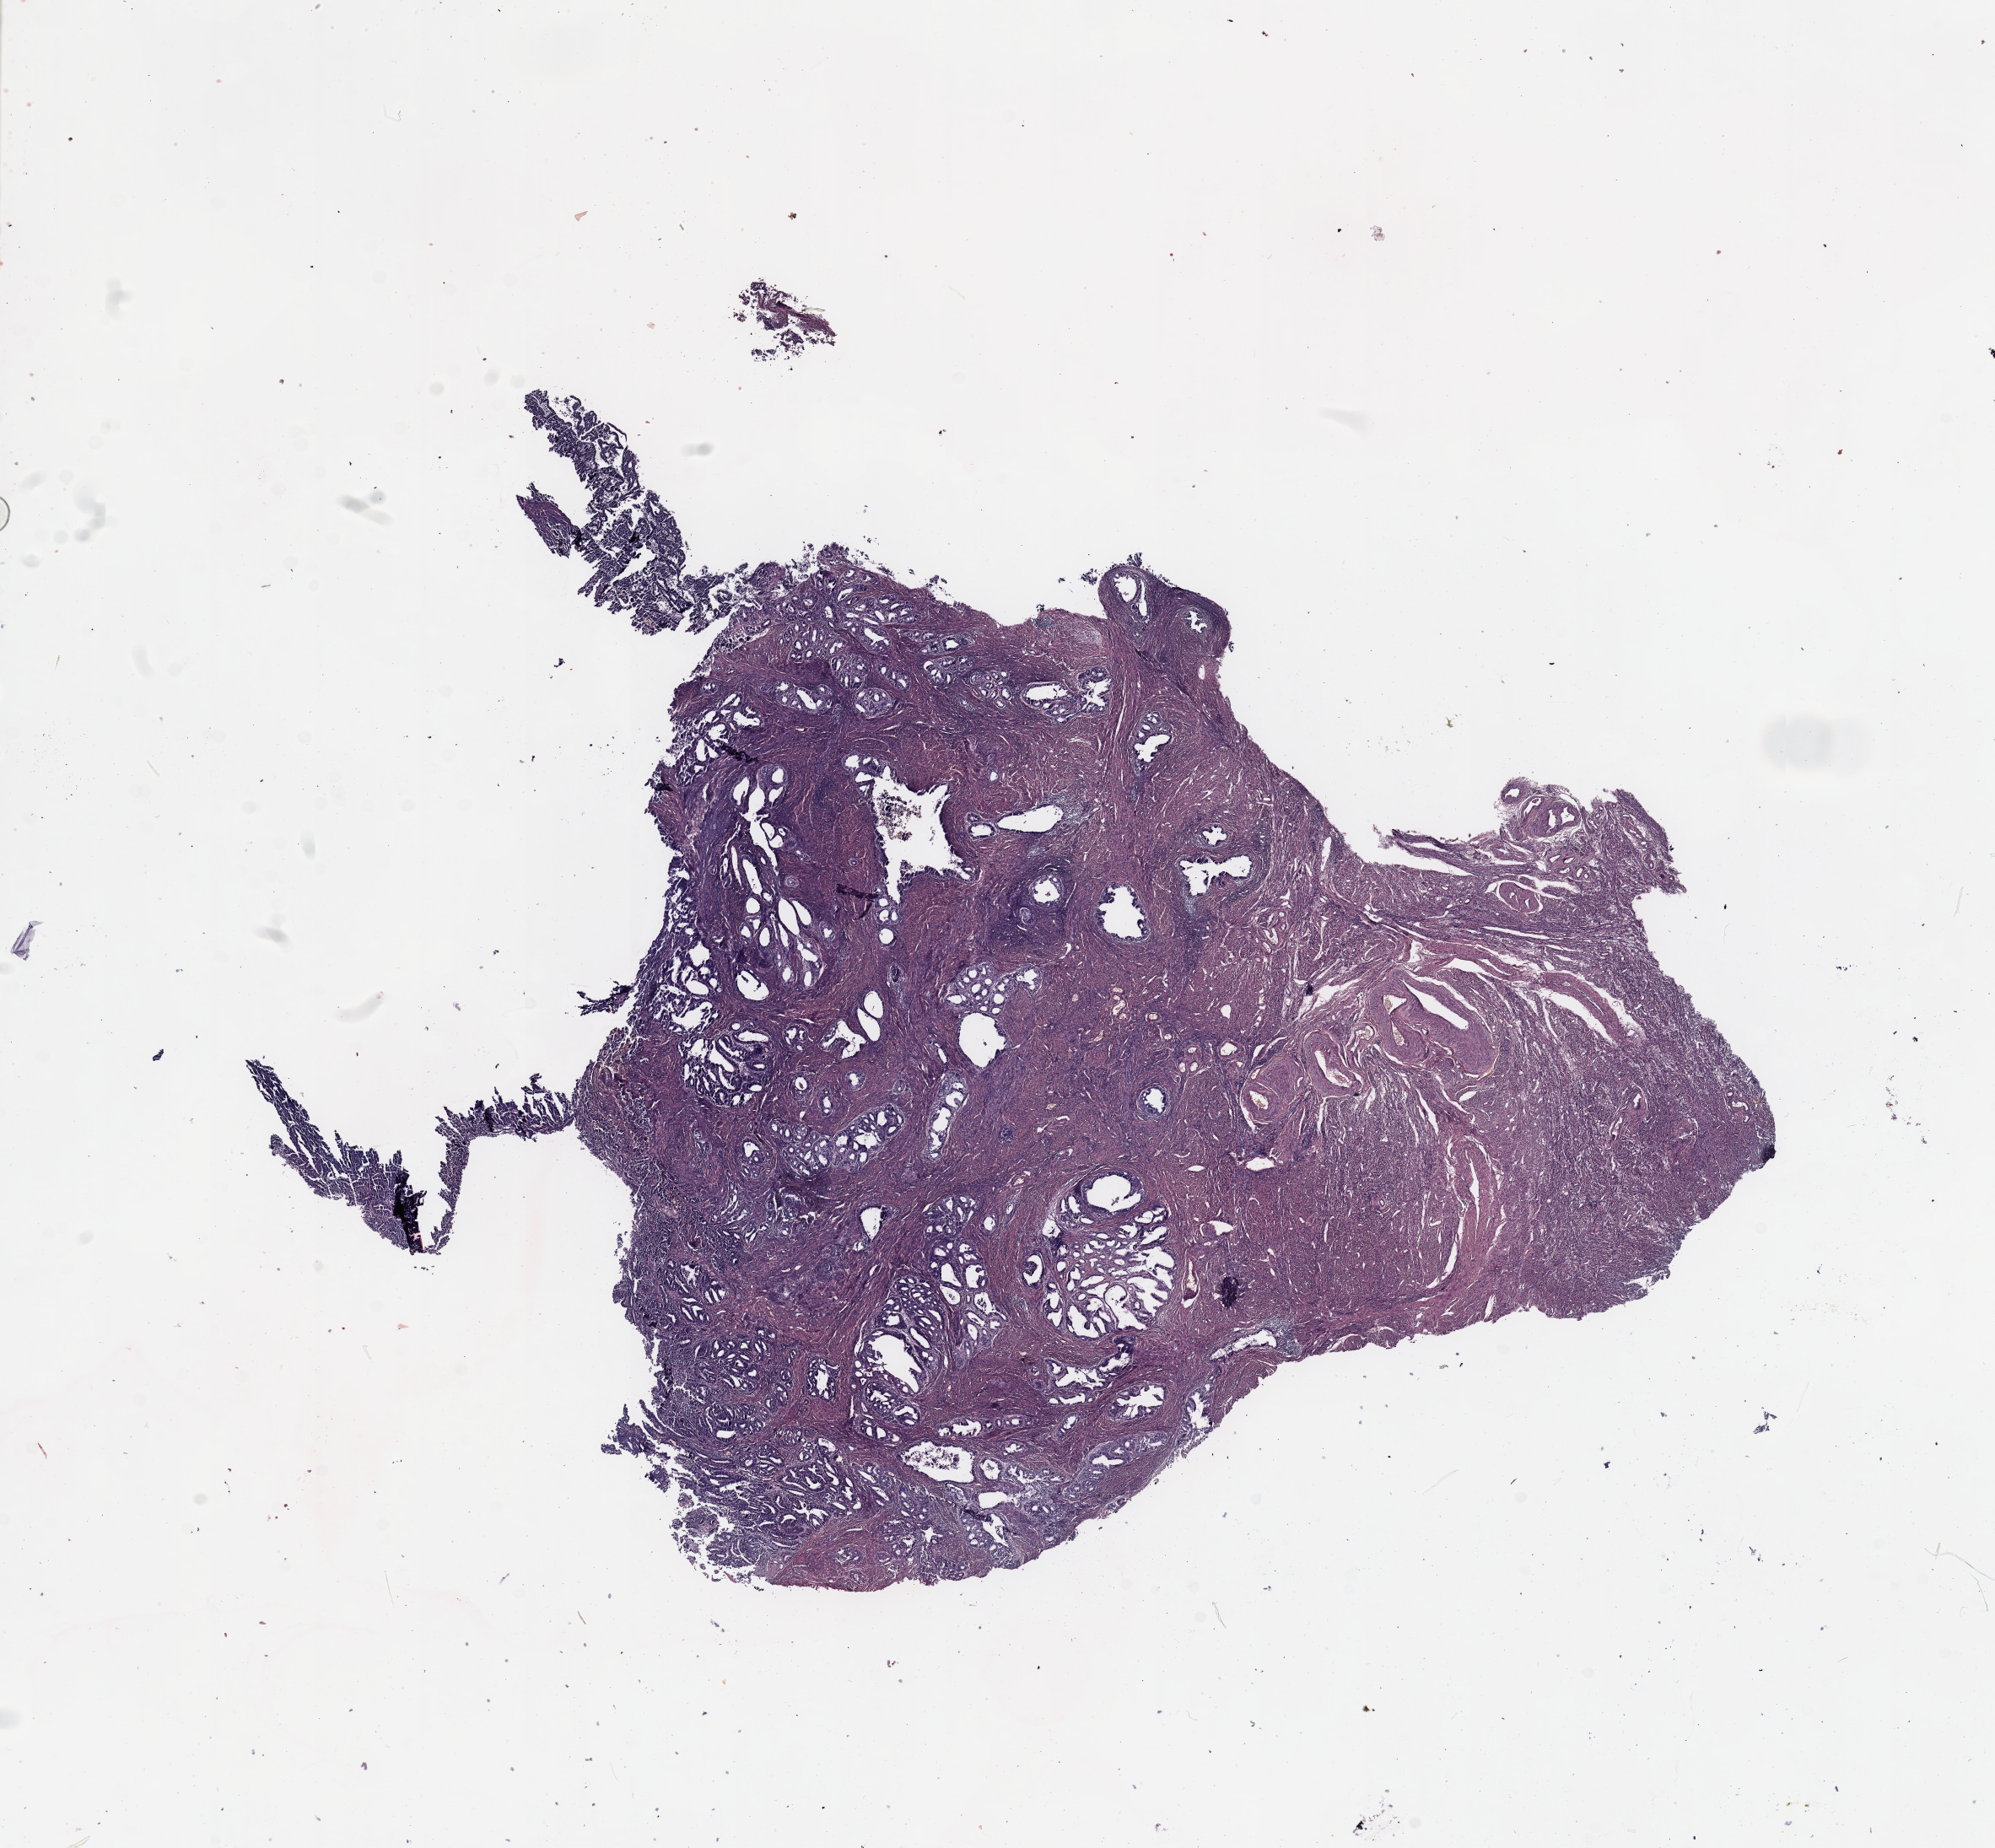
Whole-slide histology image, Hematoxylin and eosin (H&E) stained, shown as a low-resolution overview of the whole scanned area (about 18.7 x 17.3 mm, from a 20x scan), tumour tissue sample, sampled site: uterus. Female, 67 y/o.
Histologic diagnosis: Endometrioid adenocarcinoma, NOS.